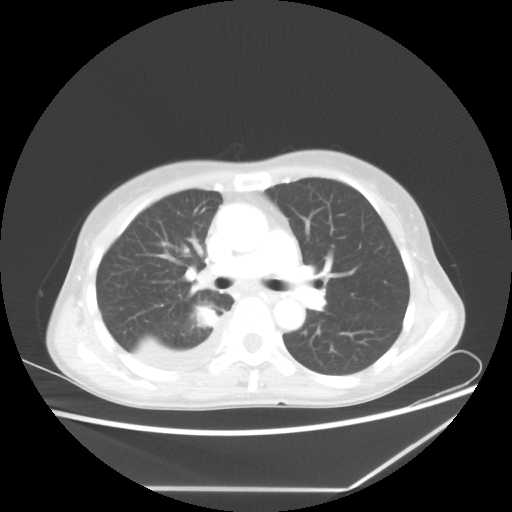
Chest CT, one axial slice. Slice 36 of 60 in the series (ordered by position). Reconstruction kernel STANDARD. 80 kVp. Lung window (W 1500 / L -600 HU). 5 mm slice thickness. 512 × 512 image matrix. Female patient, age 59 years. From the clinical record (not read from this slice): clinical TNM (as recorded): T1c N1 M1.
Outlined on this slice (bounding box drawn by a radiologist):
- lung tumour (recorded histology: adenocarcinoma): bounding box <194,303,218,327> (left, top, right, bottom; pixels)